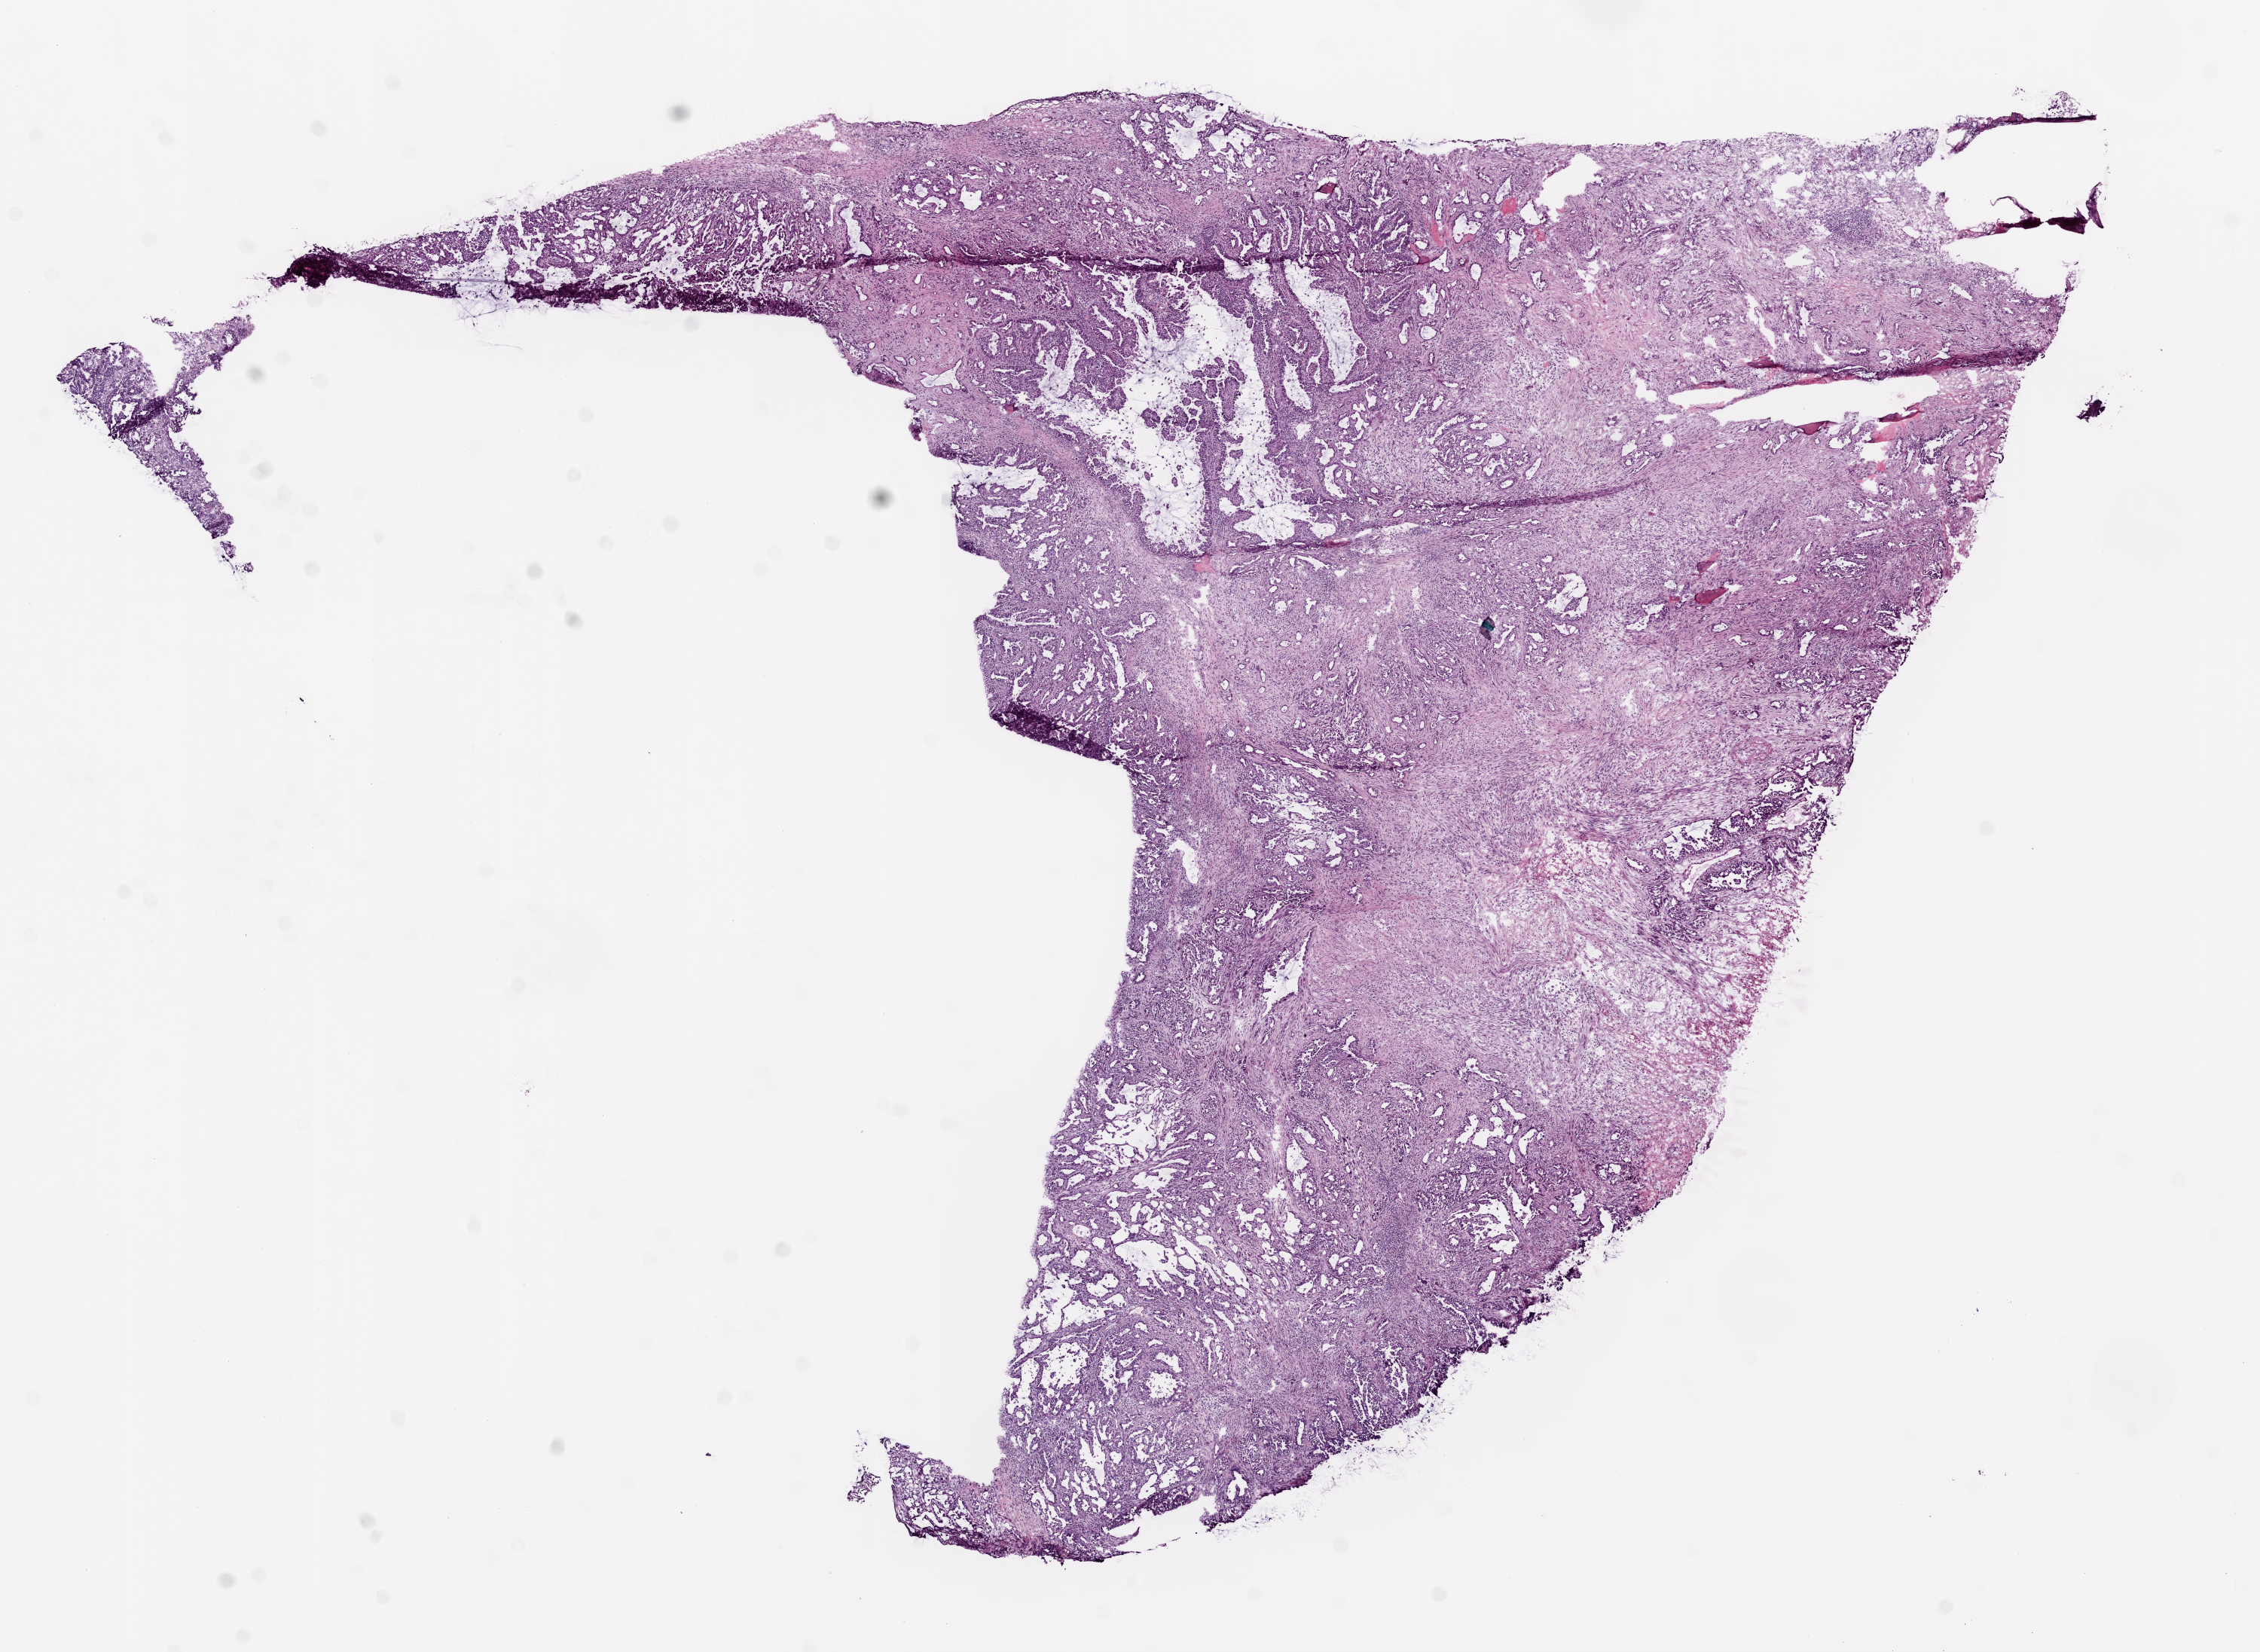
H&E whole-slide image — whole scanned area (about 12.0 x 8.8 mm, acquisition: 20x scan) shown as a low-resolution overview; frozen section from the bottom of the tissue portion; primary tumour sample from the lung. Female patient; age at initial diagnosis 70 years. Slide review estimates, as recorded: tumour cells 60%, tumour nuclei 60%, normal cells 0%, stromal cells 40%, necrosis 2%. Infiltration values recorded for this section: lymphocyte infiltration 9%, monocyte infiltration 1%.
Diagnosis: Adenocarcinoma with mixed subtypes (middle lobe, lung). AJCC pathologic stage: IV (6th edition).